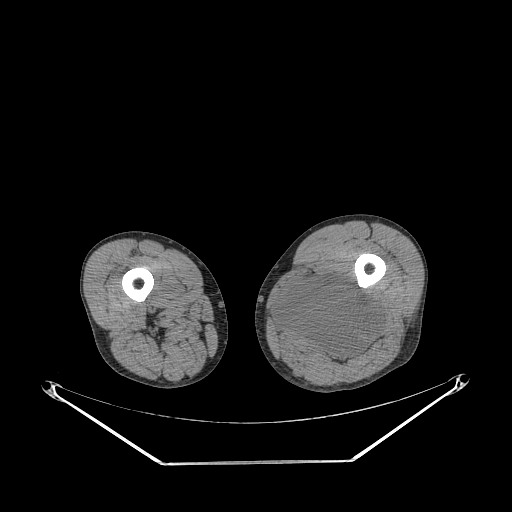
CT of an extremity soft-tissue mass (from a PET/CT study), one axial slice. Slice 230 of 267 in the series (ordered by position). 140 kVp. Soft-tissue window (W 400 / L 40 HU). 3.75 mm slice thickness. 512 × 512 image matrix, field of view 500 × 500 mm. Male patient. From the clinical record (not read from this slice): histological type: undifferentiated pleomorphic liposarcoma; grade: high; site of the primary tumour: left thigh.
Annotated regions visible in this slice (expert contour drawn on MRI and transferred to this co-registered scan by the dataset authors):
- gross tumour volume including surrounding oedema: bounding box <274,276,382,362> (left, top, right, bottom; pixels)
- gross tumour volume (mass): <276,276,382,362>